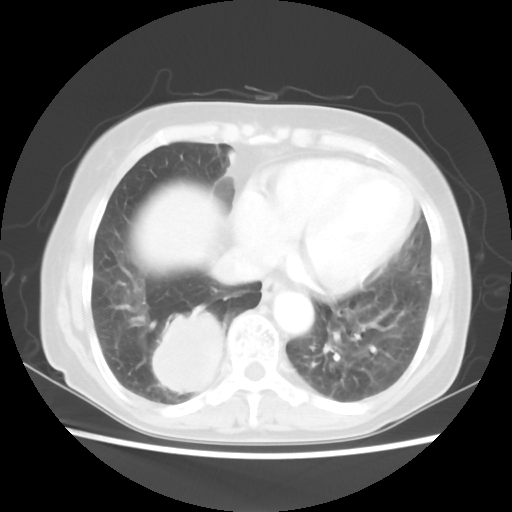
Chest CT, one axial slice; position 20 of 56 along the scan axis; reconstruction kernel STANDARD; 120 kVp; lung window (W 1500 / L -600 HU); 5 mm slice thickness; 512 × 512 image matrix. Female patient, age 66 years. From the clinical record (not read from this slice): clinical TNM (as recorded): T2 N3 M0.
Outlined on this slice (bounding box drawn by a radiologist):
- lung tumour (recorded histology: small cell carcinoma): bounding box (x1, y1, x2, y2) in pixels: (146, 295, 249, 415)